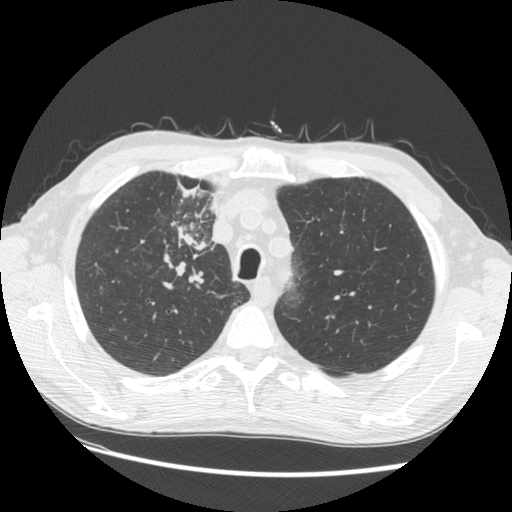
Chest CT (low-dose screening protocol), one axial image; third annual screen; lung window (W 1500 / L -600 HU); slice 28 of 133 in the series. Male participant, aged 73 years at enrolment.
- Expert-annotated lung lesion, bounding box [x1, y1, x2, y2] px = [141, 180, 232, 281].
- The screening reader recorded 4 non-calcified nodules or masses ≥4 mm on this exam (right upper lobe, right upper lobe, right upper lobe, left lower lobe); which of them this box marks is not recorded.
- Official screen result: positive, other.
- Lung cancer was diagnosed 48 days after this screen: squamous cell carcinoma, NOS, right upper lobe, poorly differentiated (G3), stage IIIB (AJCC 6th edition), 56 mm at pathology.